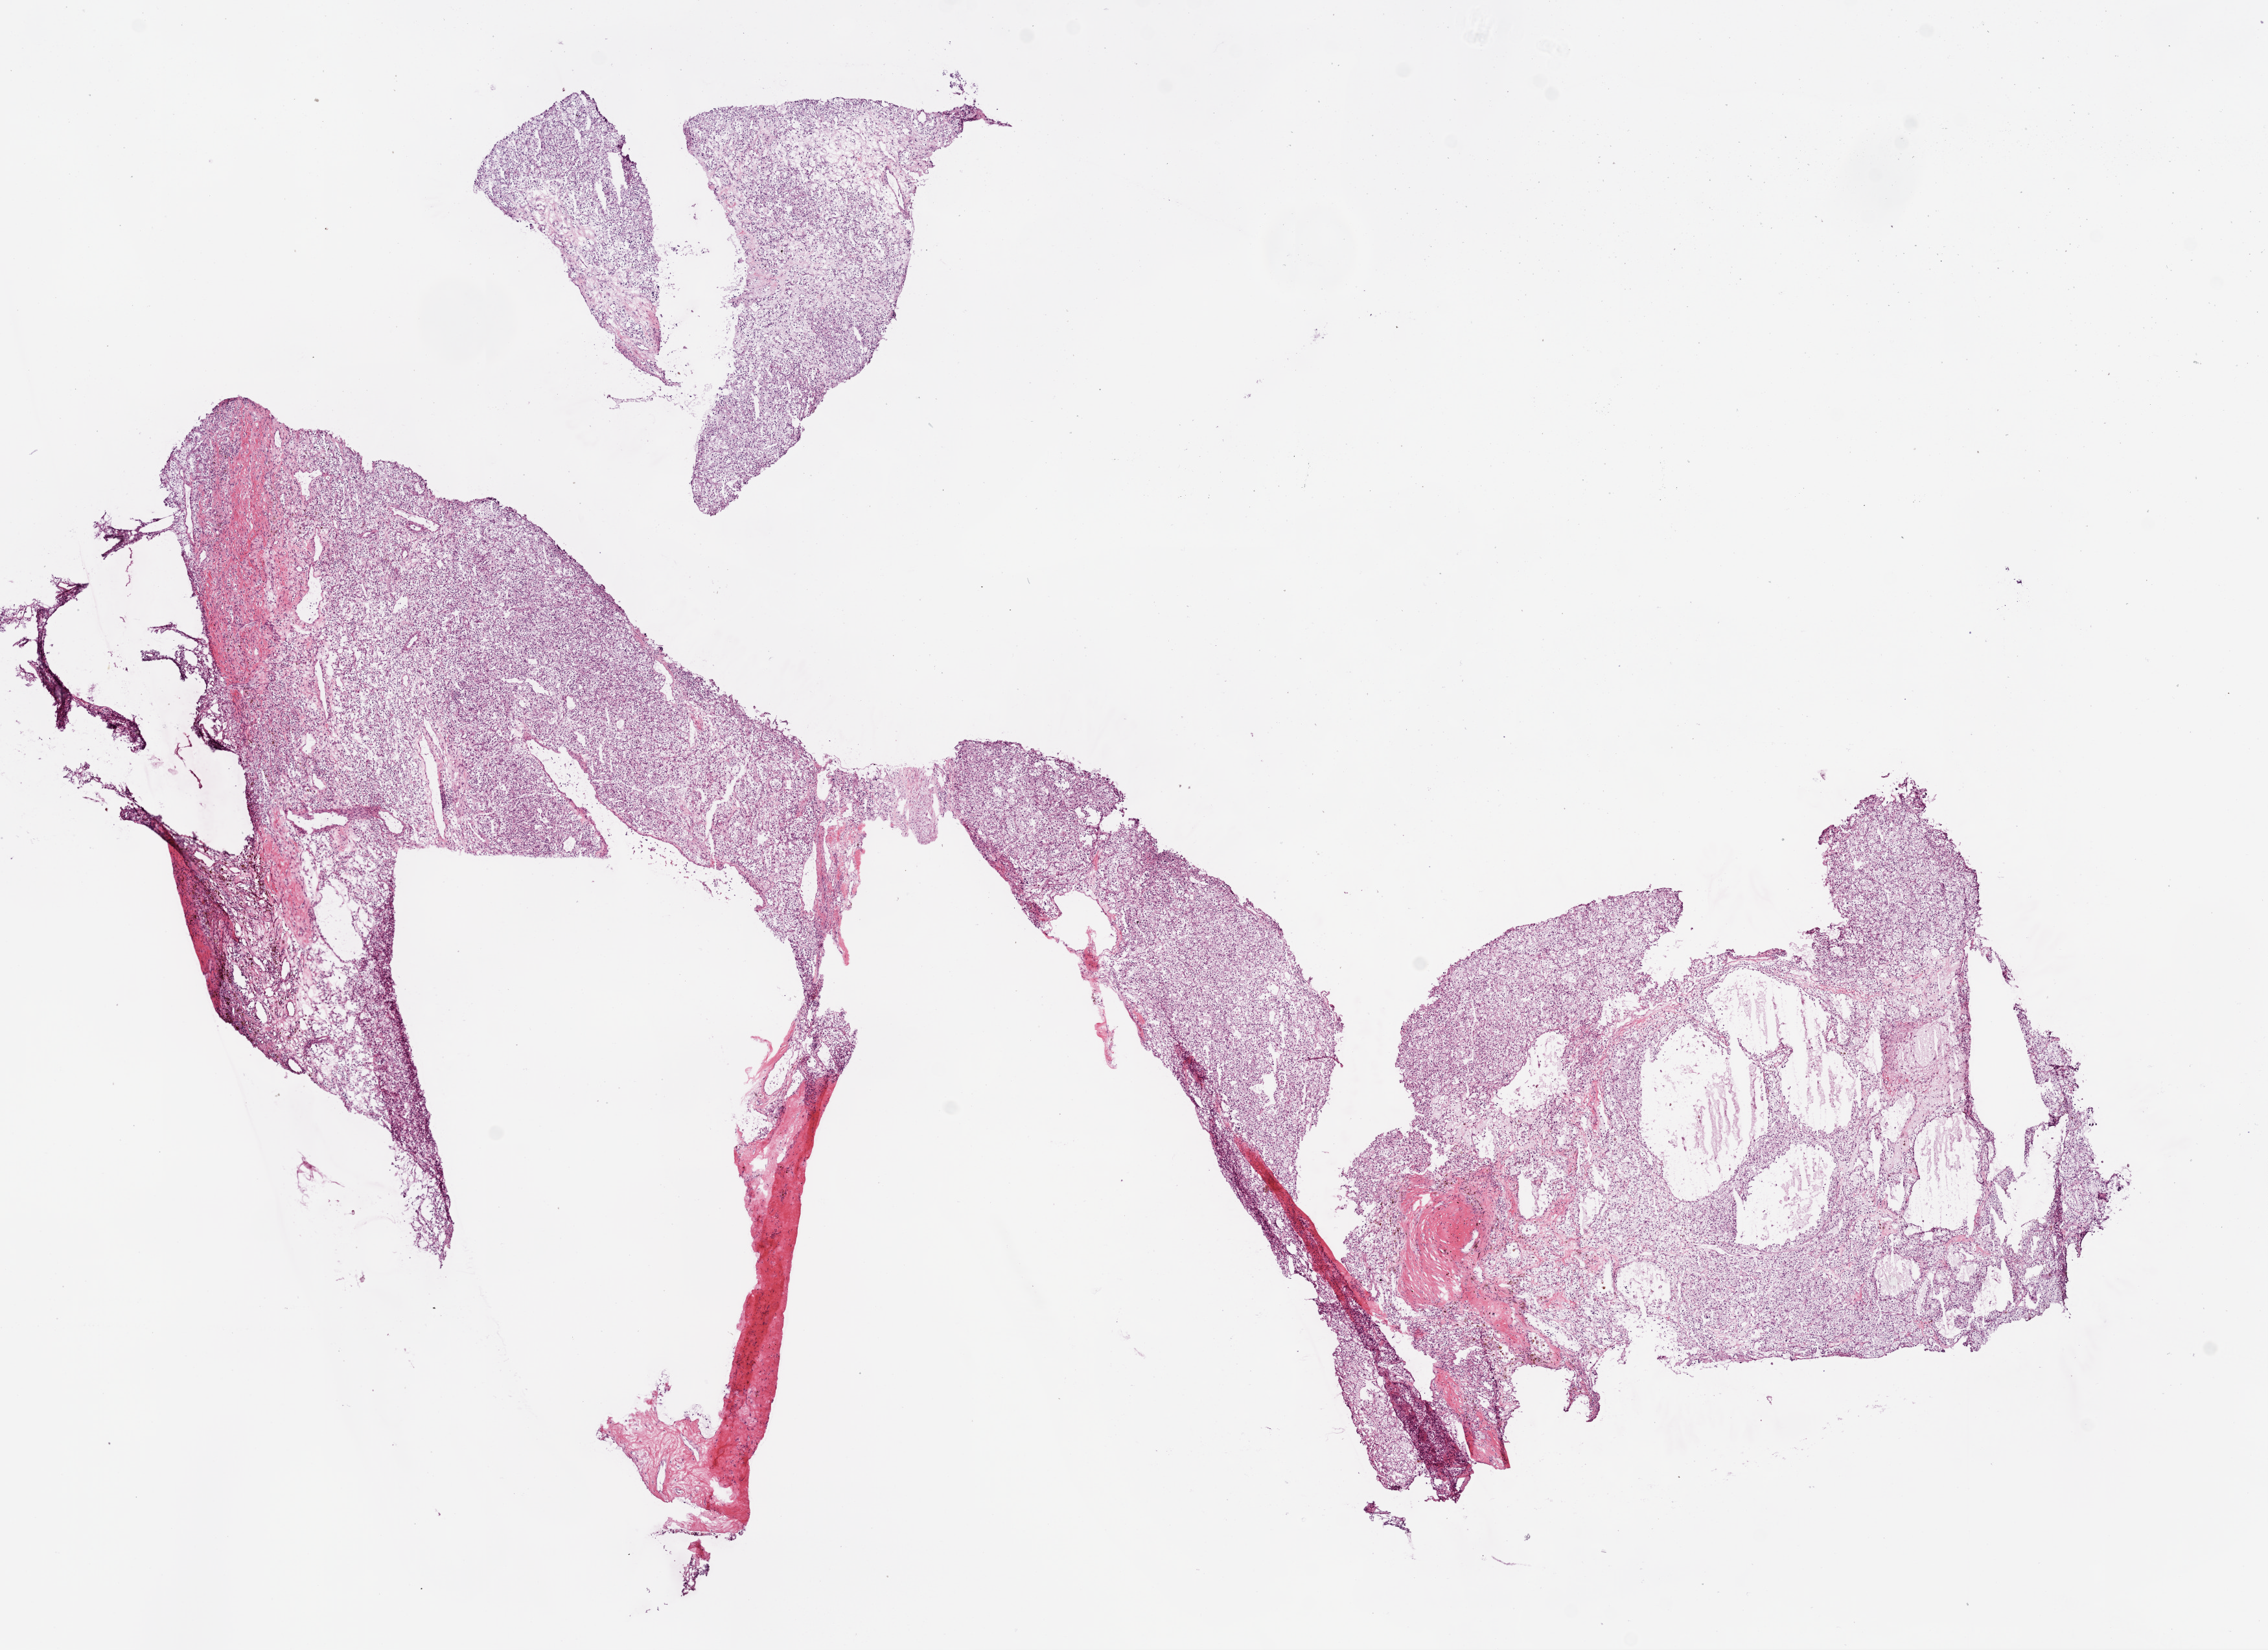
H&E-stained whole-slide image — shown as a low-resolution overview of the whole scanned area (about 14.0 x 10.2 mm), frozen section from the bottom of the tissue portion, sample: primary tumour, kidney. Male, age 40 years at initial diagnosis. Histologic grade: G3 (poorly differentiated). Slide review estimates, as recorded: tumour cells 85%, tumour nuclei 85%, normal cells 0%, stromal cells 15%, necrosis 0%.
Laterality: right. AJCC pathologic stage: I. Diagnosis: Clear cell adenocarcinoma, NOS.